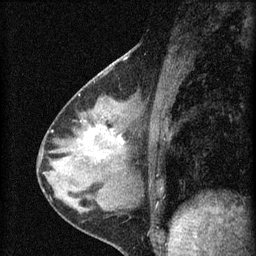
Breast MRI (dynamic contrast-enhanced), one sagittal slice; position 24 of 60 along the scan axis; dynamic contrast-enhanced series, image 2 of 4 at this slice position (ordered by acquisition); 1.5 T; TE 4.2 ms, TR 8.2 ms; 2 mm slice thickness; 256 × 256 image matrix, field of view 180 × 180 mm. Patient: female, 37 years.
Structures marked on this image (semi-automatic segmentation, software-assisted and operator-edited):
- analysis volume of interest (the breast-tissue region the enhancement analysis was run in; not a lesion): box from (x=77, y=116) to (x=127, y=175) px
- tumour enhancement mask (voxels above the 70 % enhancement threshold inside the analysis volume of interest): (x=93, y=128)–(x=124, y=157)